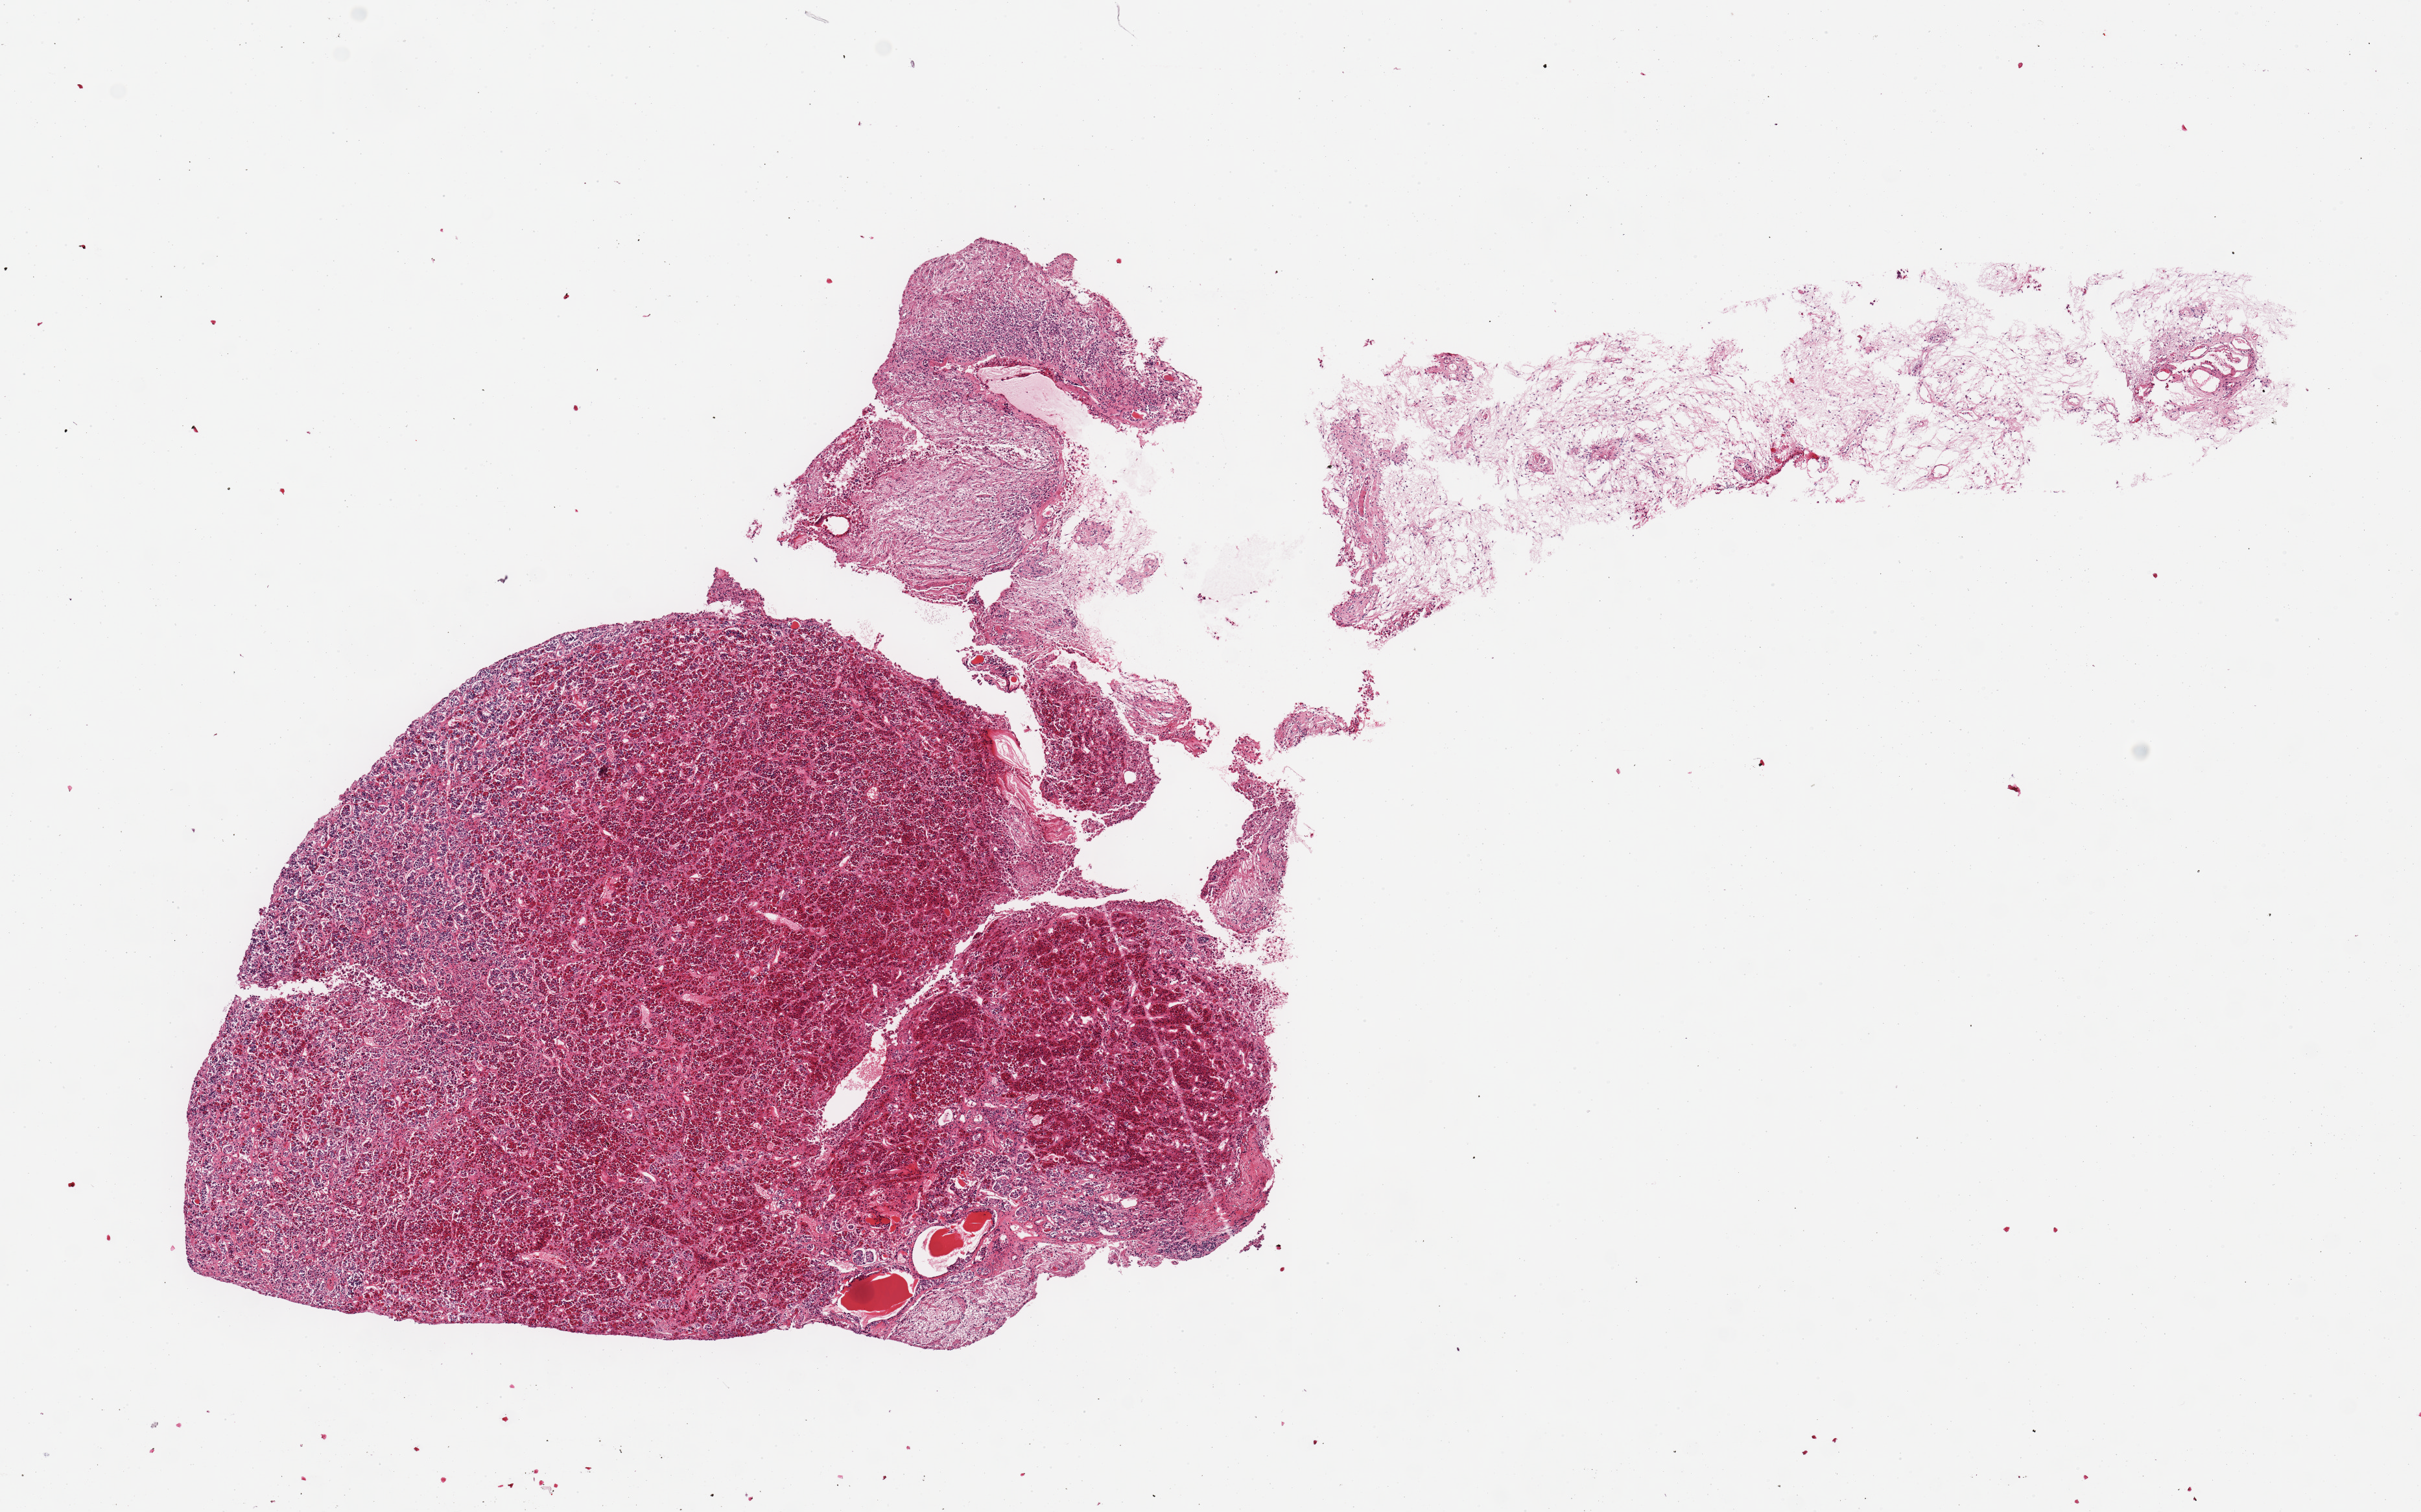
Digitized haematoxylin and eosin-stained section — a low-resolution overview of the entire scanned area, about 14.8 x 9.2 mm (slide scanned at 20x); PAXgene-fixed paraffin-embedded (PFPE) section; target tissue: pituitary; donor tissue sample. Male donor.
- pathologist's review note for this sample: 1 piece, mainly adenohypophysis; 2x1mm nubbin of neurohypophysis; Remainder is fibrous tissue